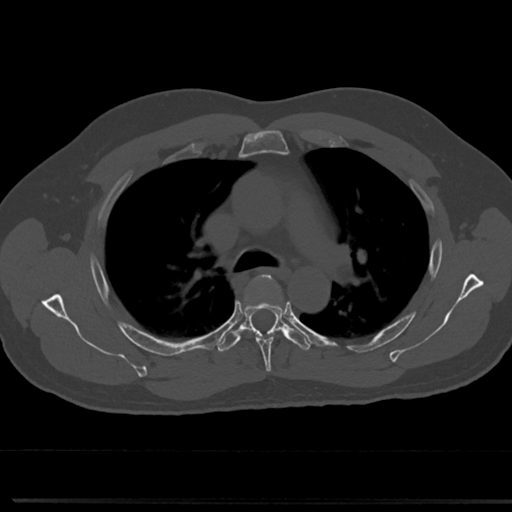
CT including the spine, one axial slice; slice 520 of 817 in the series (ordered by position); reconstruction kernel Br40s/3; bone window (W 1800 / L 400 HU); 512 × 512 image matrix, field of view 355 × 355 mm. Patient: male, 61 years. From the clinical record (not read from this slice): primary cancer: prostate.
Outlined on this slice (semi-automatic segmentation, software-assisted and operator-edited):
- T4 vertebra: bounding box (x1, y1, x2, y2) in pixels: (240, 275, 287, 362)
- T5 vertebra: (223, 308, 310, 349)